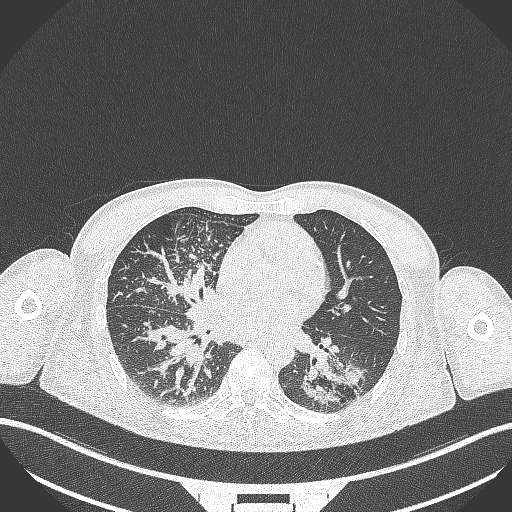
Chest CT, one axial slice; slice 147 of 348 in the series (ordered by position); 120 kVp; lung window (W 1500 / L -600 HU); 512 × 512 image matrix, field of view 400 × 400 mm. Patient: male, 49 years. From the clinical record (not read from this slice): clinical TNM (as recorded): T2b N1 M0.
Structures marked on this image (rectangle marked by the reading radiologist):
- lung tumour (recorded histology: adenocarcinoma): bounding box [x1, y1, x2, y2] px = [295, 348, 368, 405]